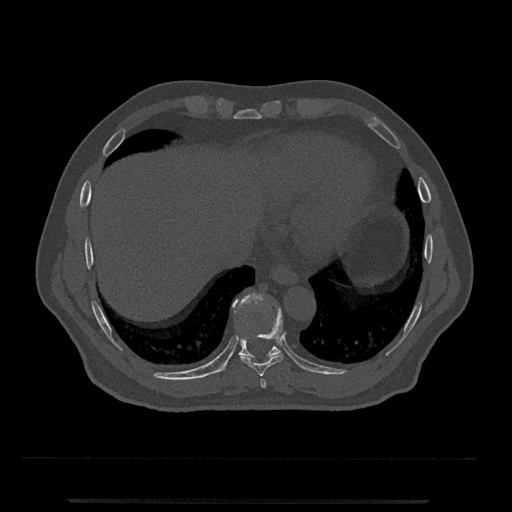
CT including the spine, one axial slice. Position 551 of 797 along the scan axis. Reconstruction kernel Br40s/3. 120 kVp. Bone window (W 1800 / L 400 HU). 0.5 mm slice thickness. 512 × 512 image matrix, field of view 419 × 419 mm. Male patient, age 63 years. From the clinical record (not read from this slice): primary cancer: prostate.
Structures marked on this image (semi-automatically segmented with operator editing):
- T10 vertebra: box from (x=220, y=293) to (x=281, y=372) px
- T8 vertebra: (x=260, y=379)–(x=266, y=388)
- T9 vertebra: (x=241, y=307)–(x=283, y=377)